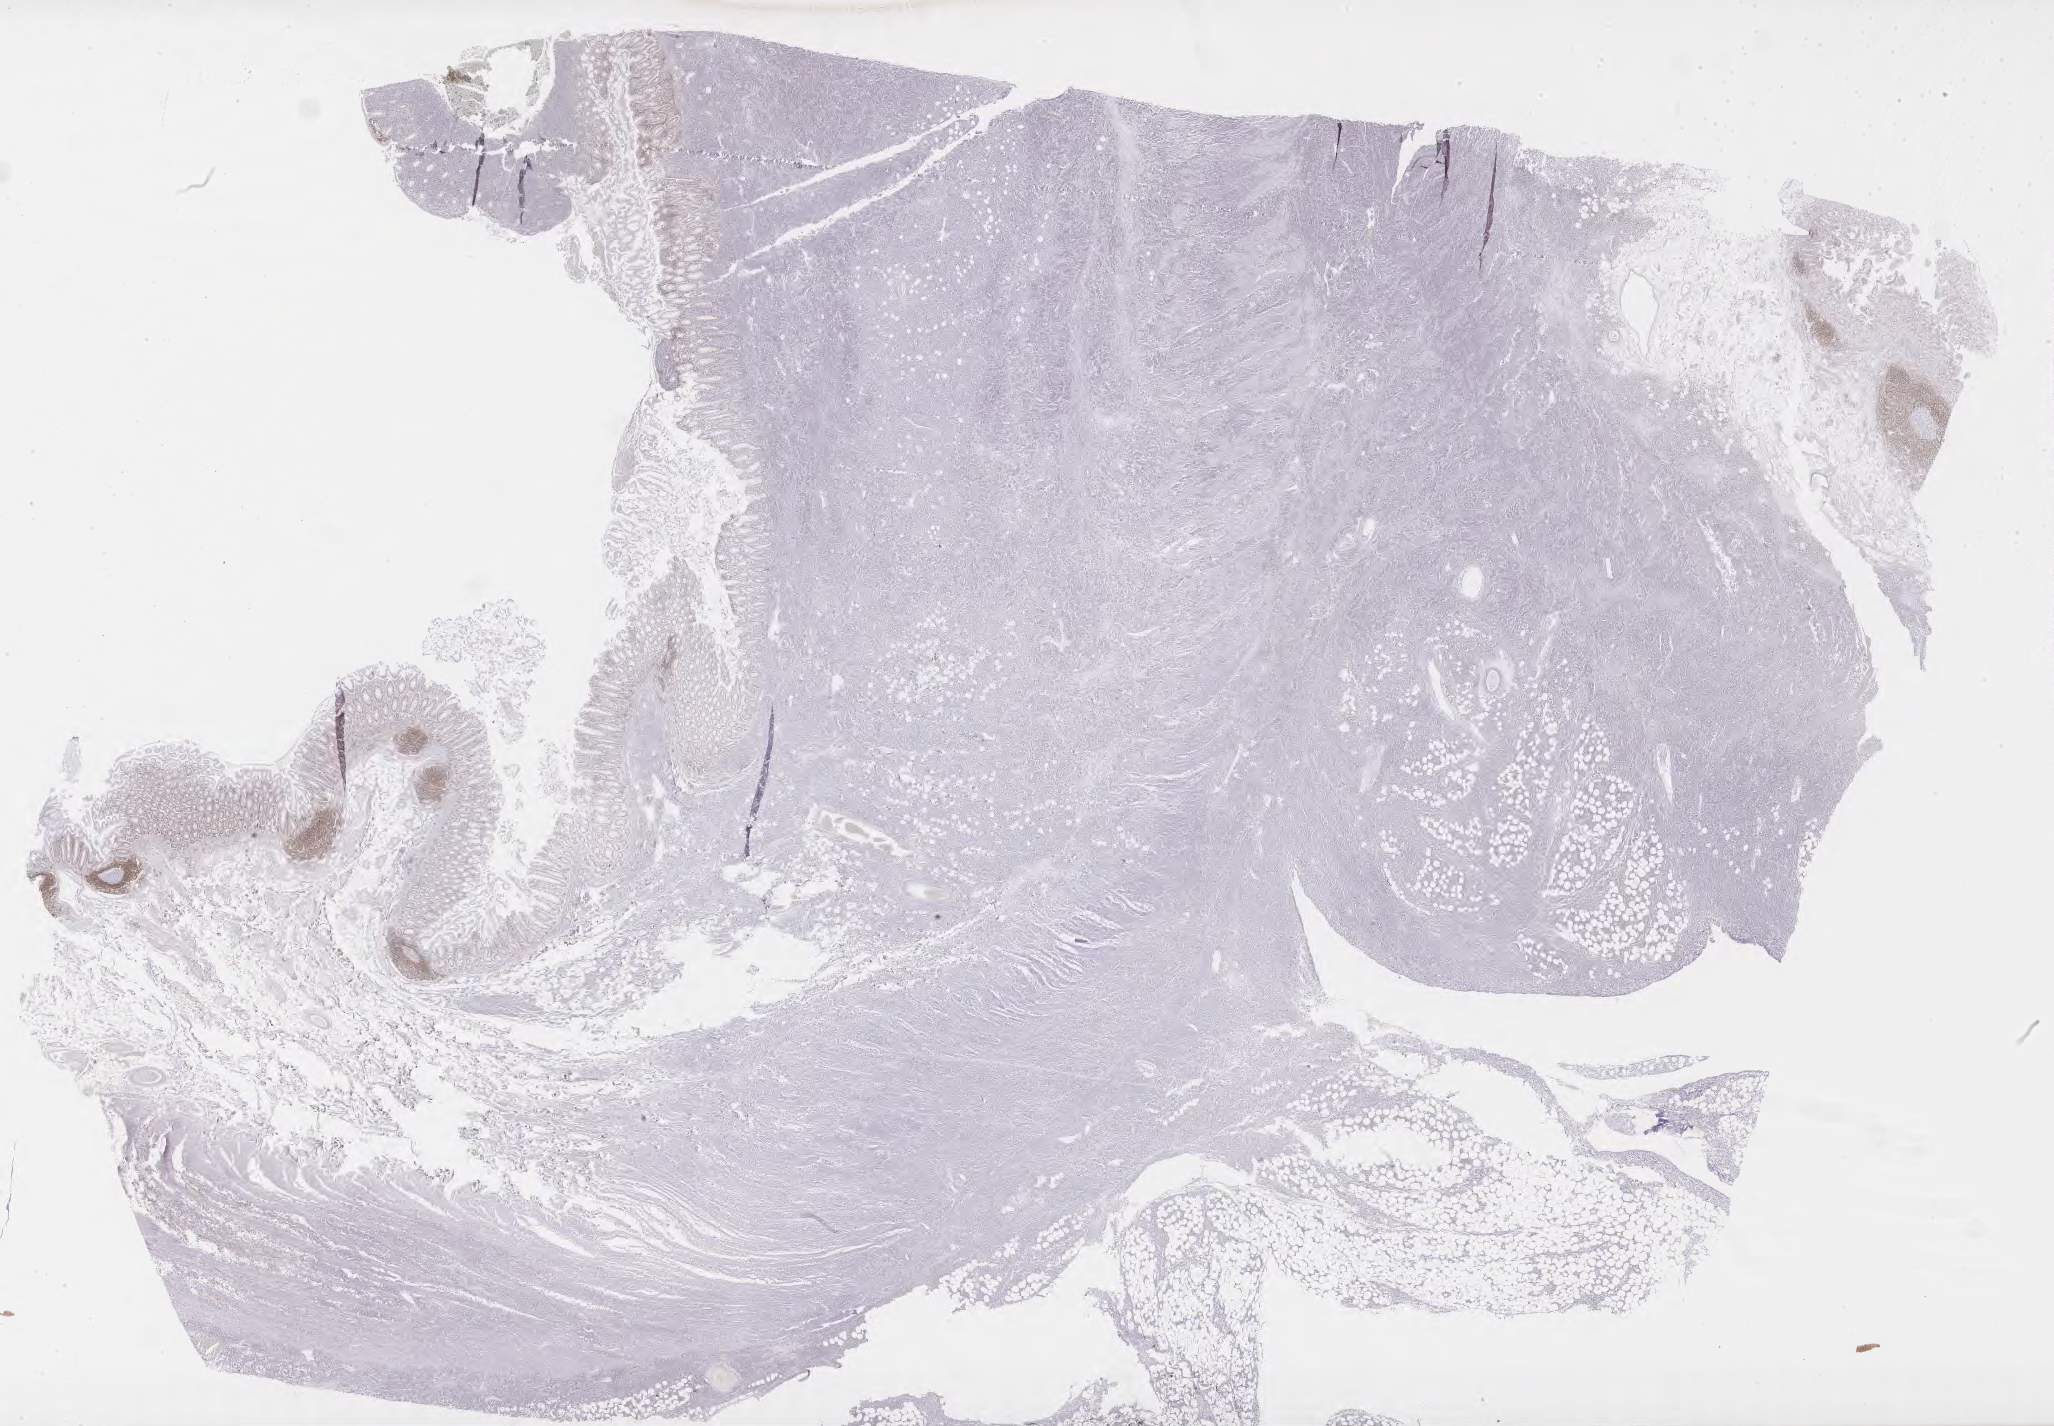
IHC for BCL2, whole-slide image — low-resolution overview of the scanned area, about 33.2 x 23.1 mm; specimen: tumor tissue. Male patient, age 56 years.
Histologic diagnosis: Burkitt lymphoma, NOS.